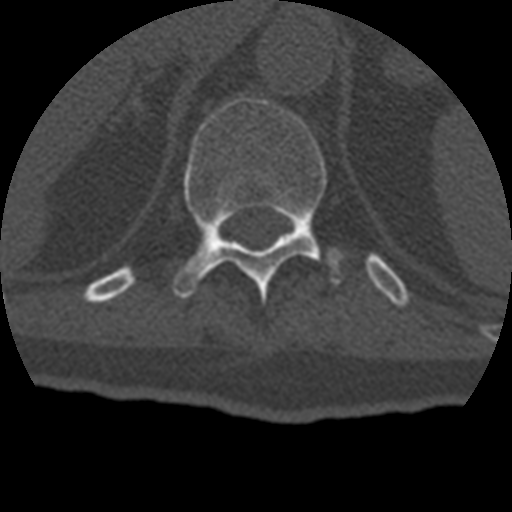
CT including the spine, one axial slice. Position 196 of 399 along the scan axis. 120 kVp. Bone window (W 1800 / L 400 HU). 1.25 mm slice thickness. 512 × 512 image matrix, field of view 160 × 160 mm. Patient age 69 years. Case-level facts recorded for this patient, not image findings: primary cancer: prostate.
Outlined on this slice (semi-automatically segmented with operator editing):
- T11 vertebra: bounding box <173,96,342,298> (left, top, right, bottom; pixels)